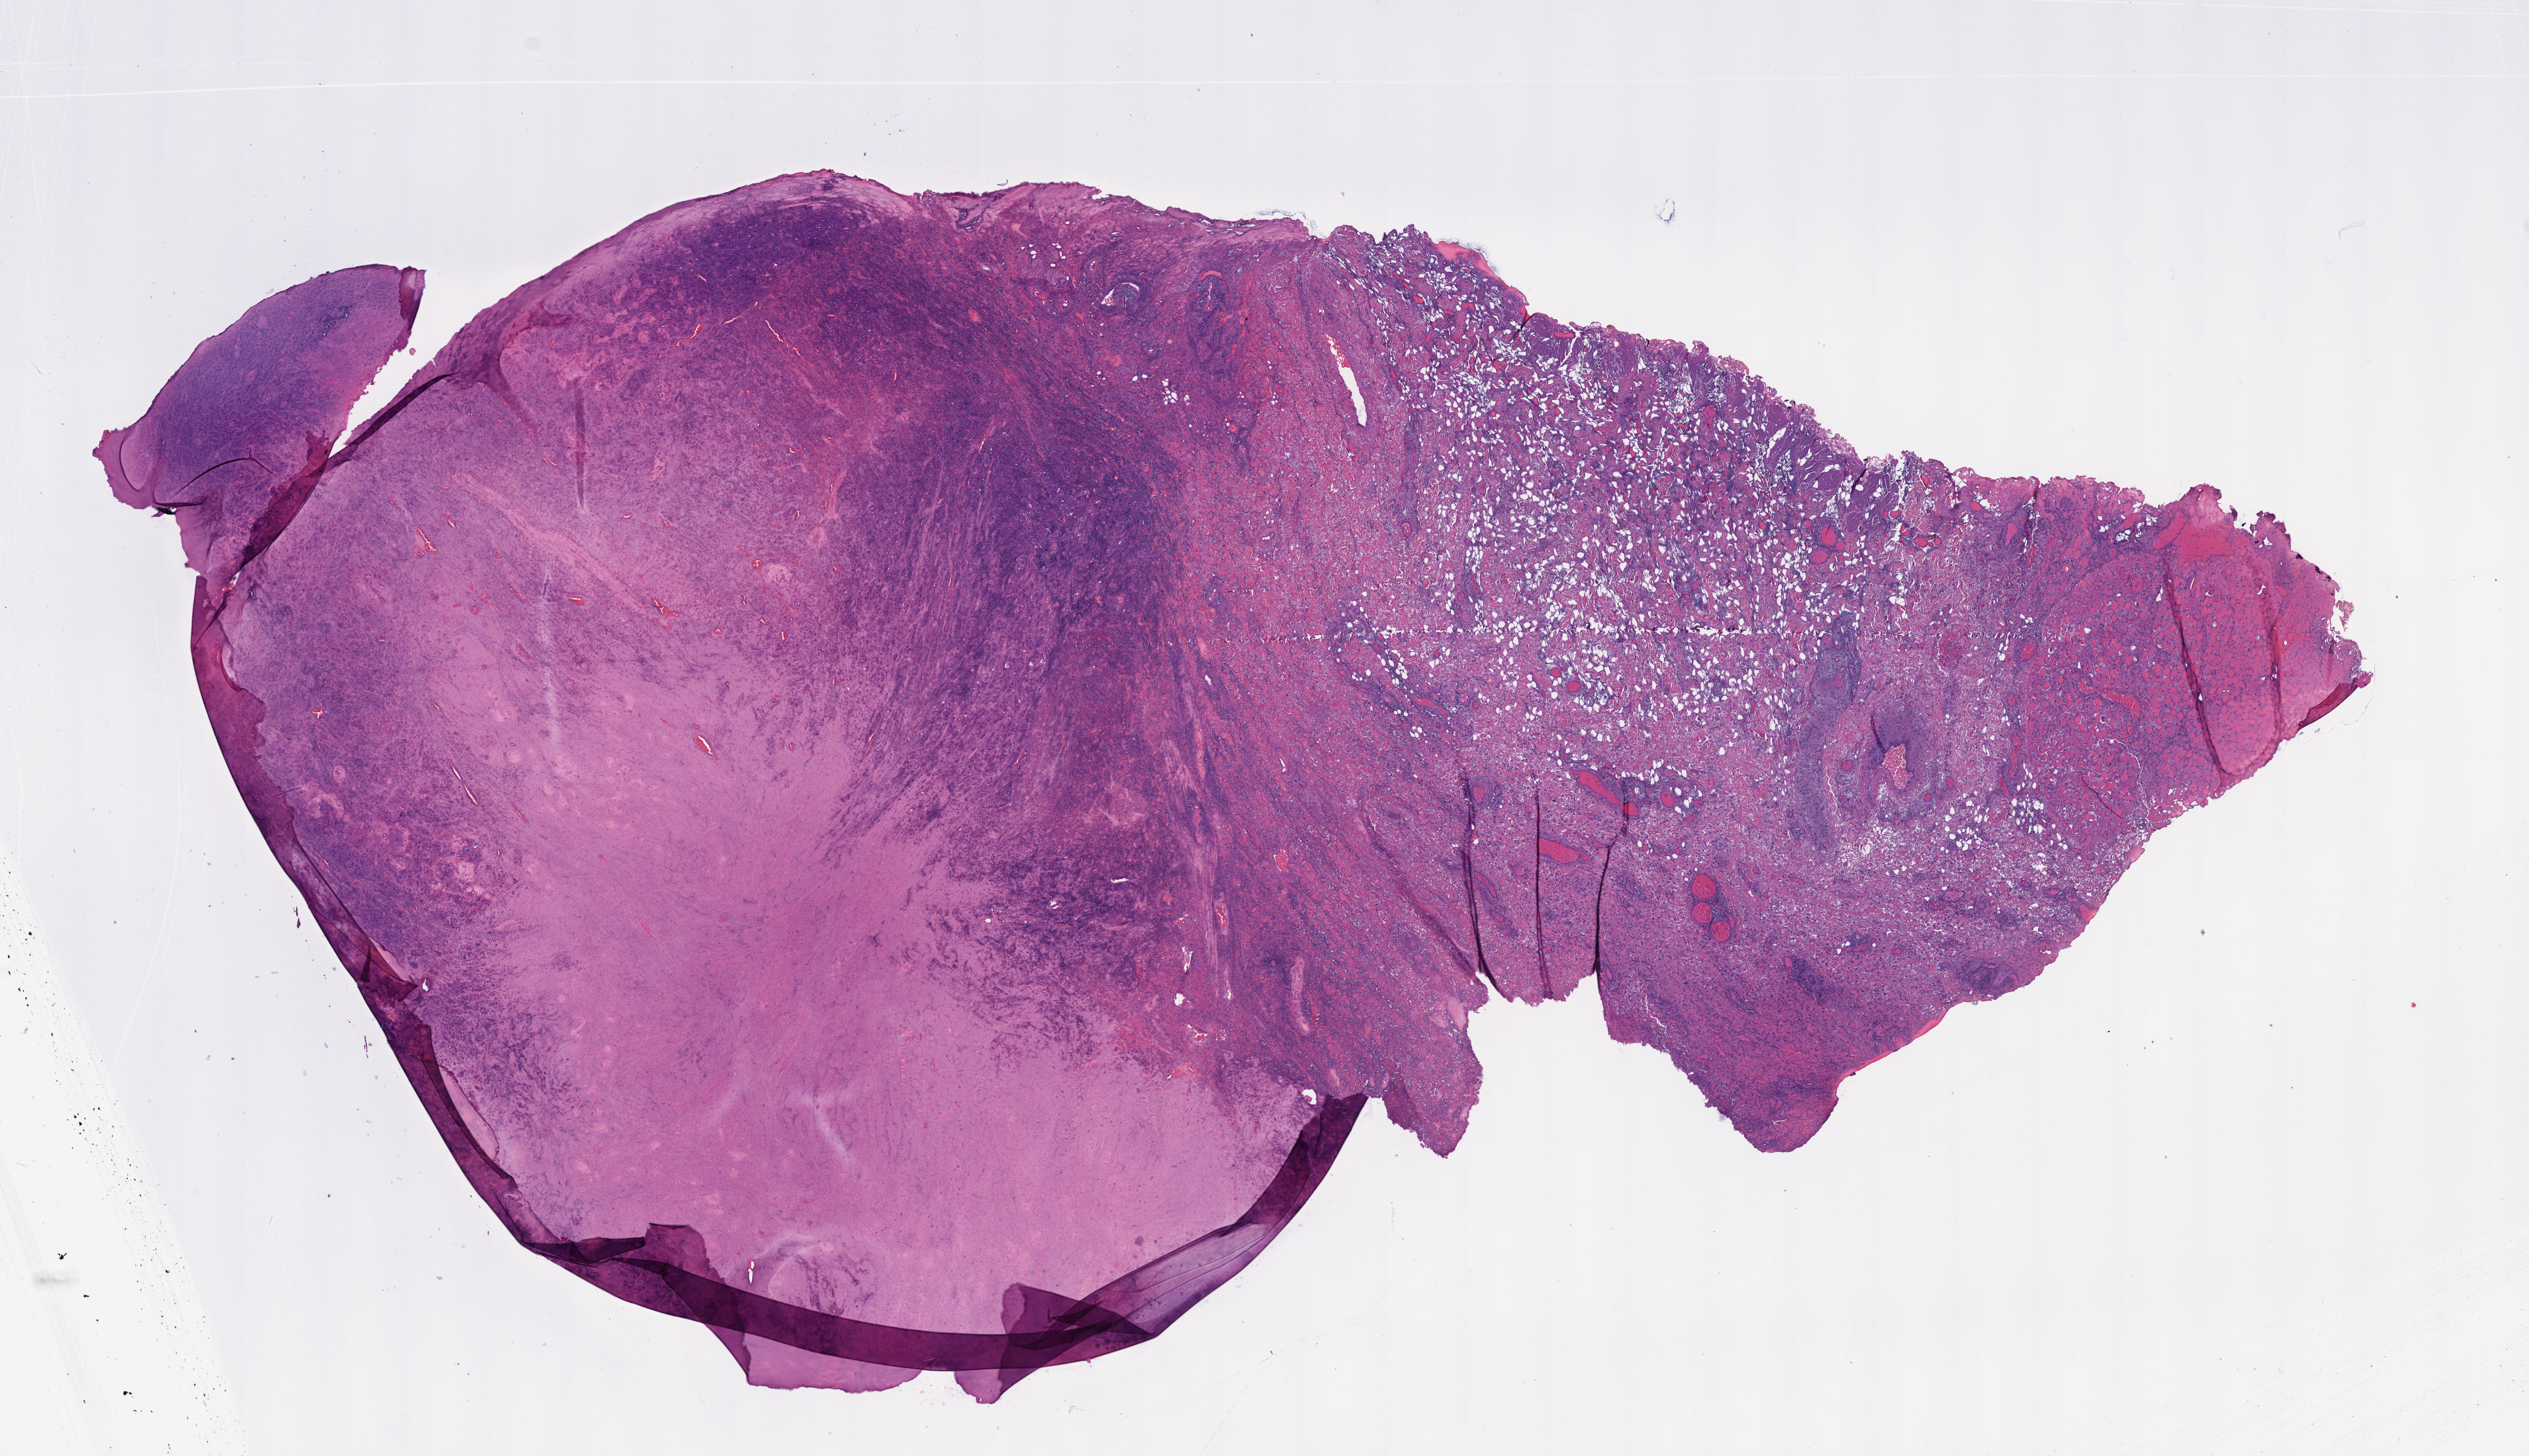
Digitized Hematoxylin and eosin (H&E) stained tissue section (whole slide), a low-resolution overview of the entire scanned area, about 15.6 x 9.0 mm (acquisition: 40x scan), FFPE section, head and neck, primary tumour sample. Female patient; age at initial diagnosis 63 years.
Diagnosis: Squamous cell carcinoma, NOS (overlapping lesion of lip, oral cavity and pharynx).